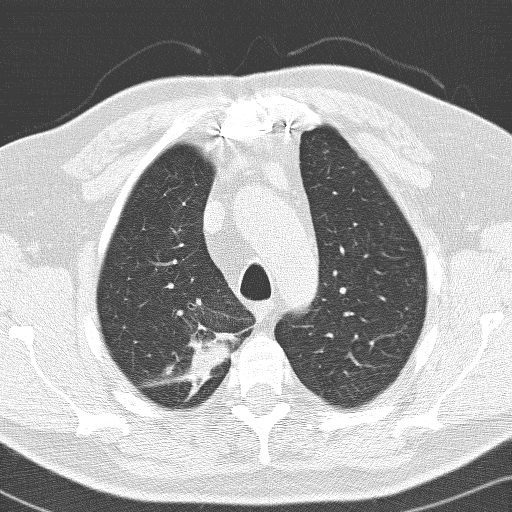
Low-dose screening chest CT, one axial slice. Slice 114 of 141 in the series (ordered by position). 120 kVp. Lung window (W 1500 / L -600 HU). 3.2 mm slice thickness. 512 × 512 image matrix, field of view 326 × 326 mm.
Outlined on this slice (expert manual segmentation):
- lesion 1 (tumor, upper lobe of right lung): bounding box (x1, y1, x2, y2) in pixels: (186, 323, 238, 400)